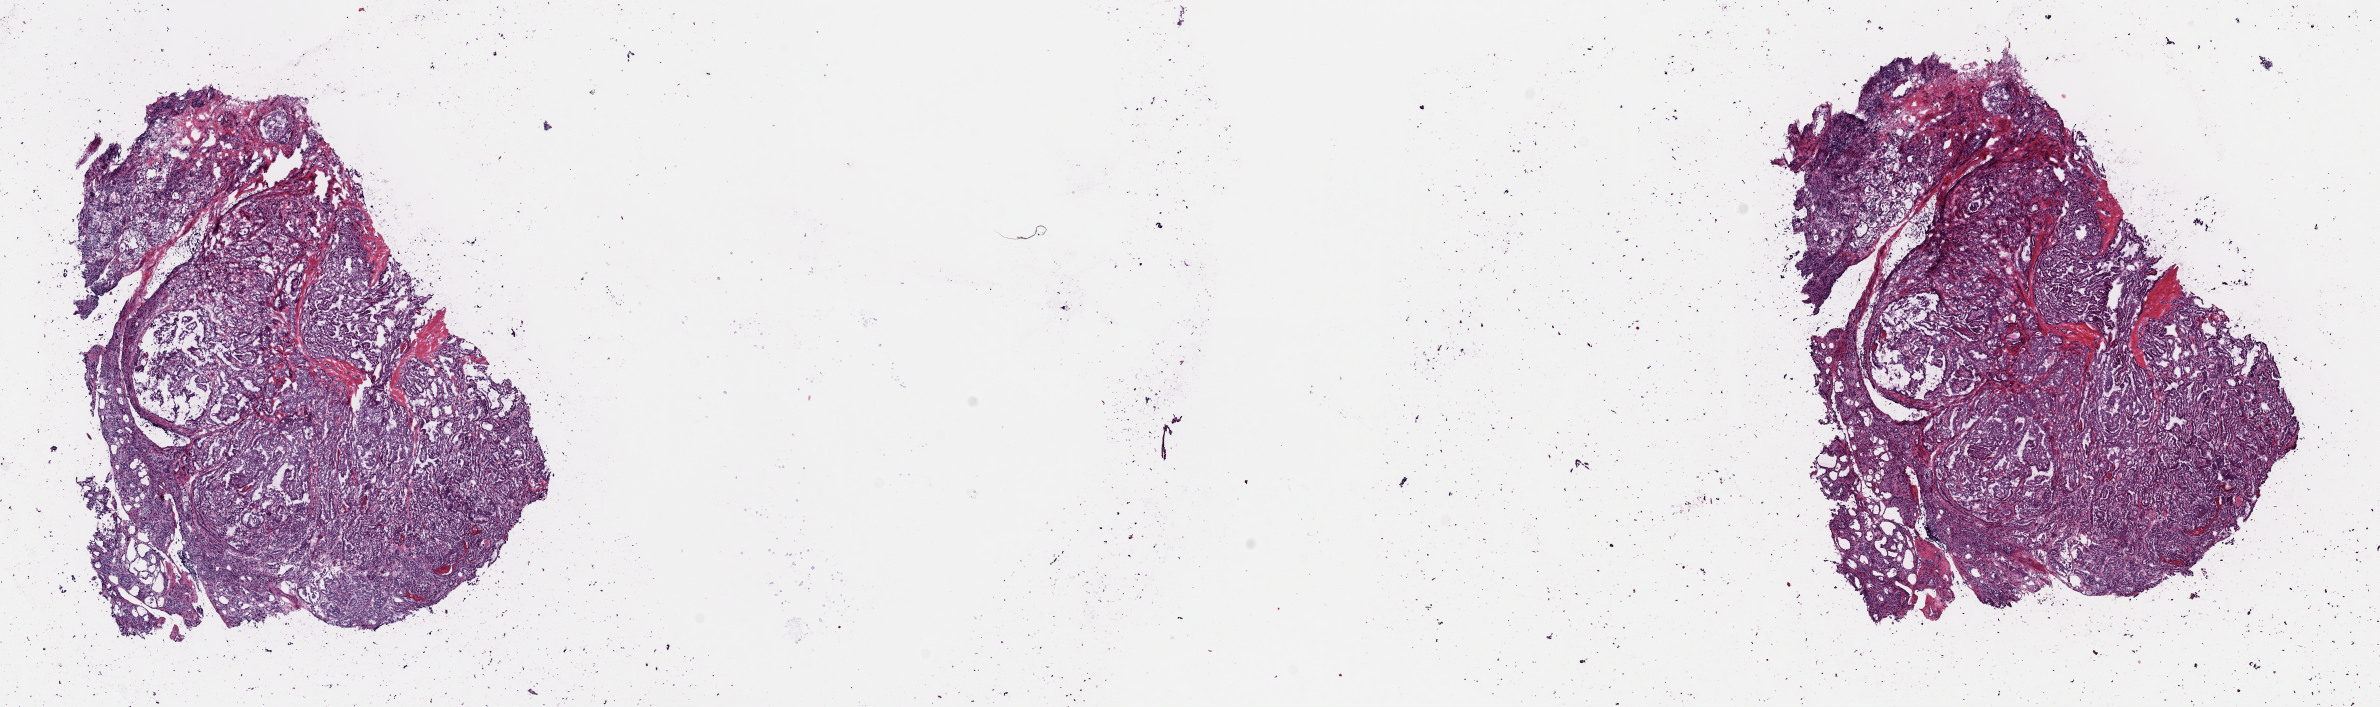
Digitized Hematoxylin and eosin (H&E) stained tissue section (whole slide), low-resolution overview of the scanned area, about 18.8 x 5.6 mm (acquisition: 40x scan). Frozen section from the top of the tissue portion. Sample: primary tumour, thyroid. Female, age 32 years at initial diagnosis. Slide review estimates, as recorded: tumour cells 70%, tumour nuclei 70%, normal cells 5%, stromal cells 25%, necrosis 0%. Infiltration values recorded for this section: lymphocyte infiltration 10%, monocyte infiltration 0%, neutrophil infiltration 0%.
* AJCC pathologic stage: I (7th edition)
* diagnosis: Papillary adenocarcinoma, NOS (thyroid gland)